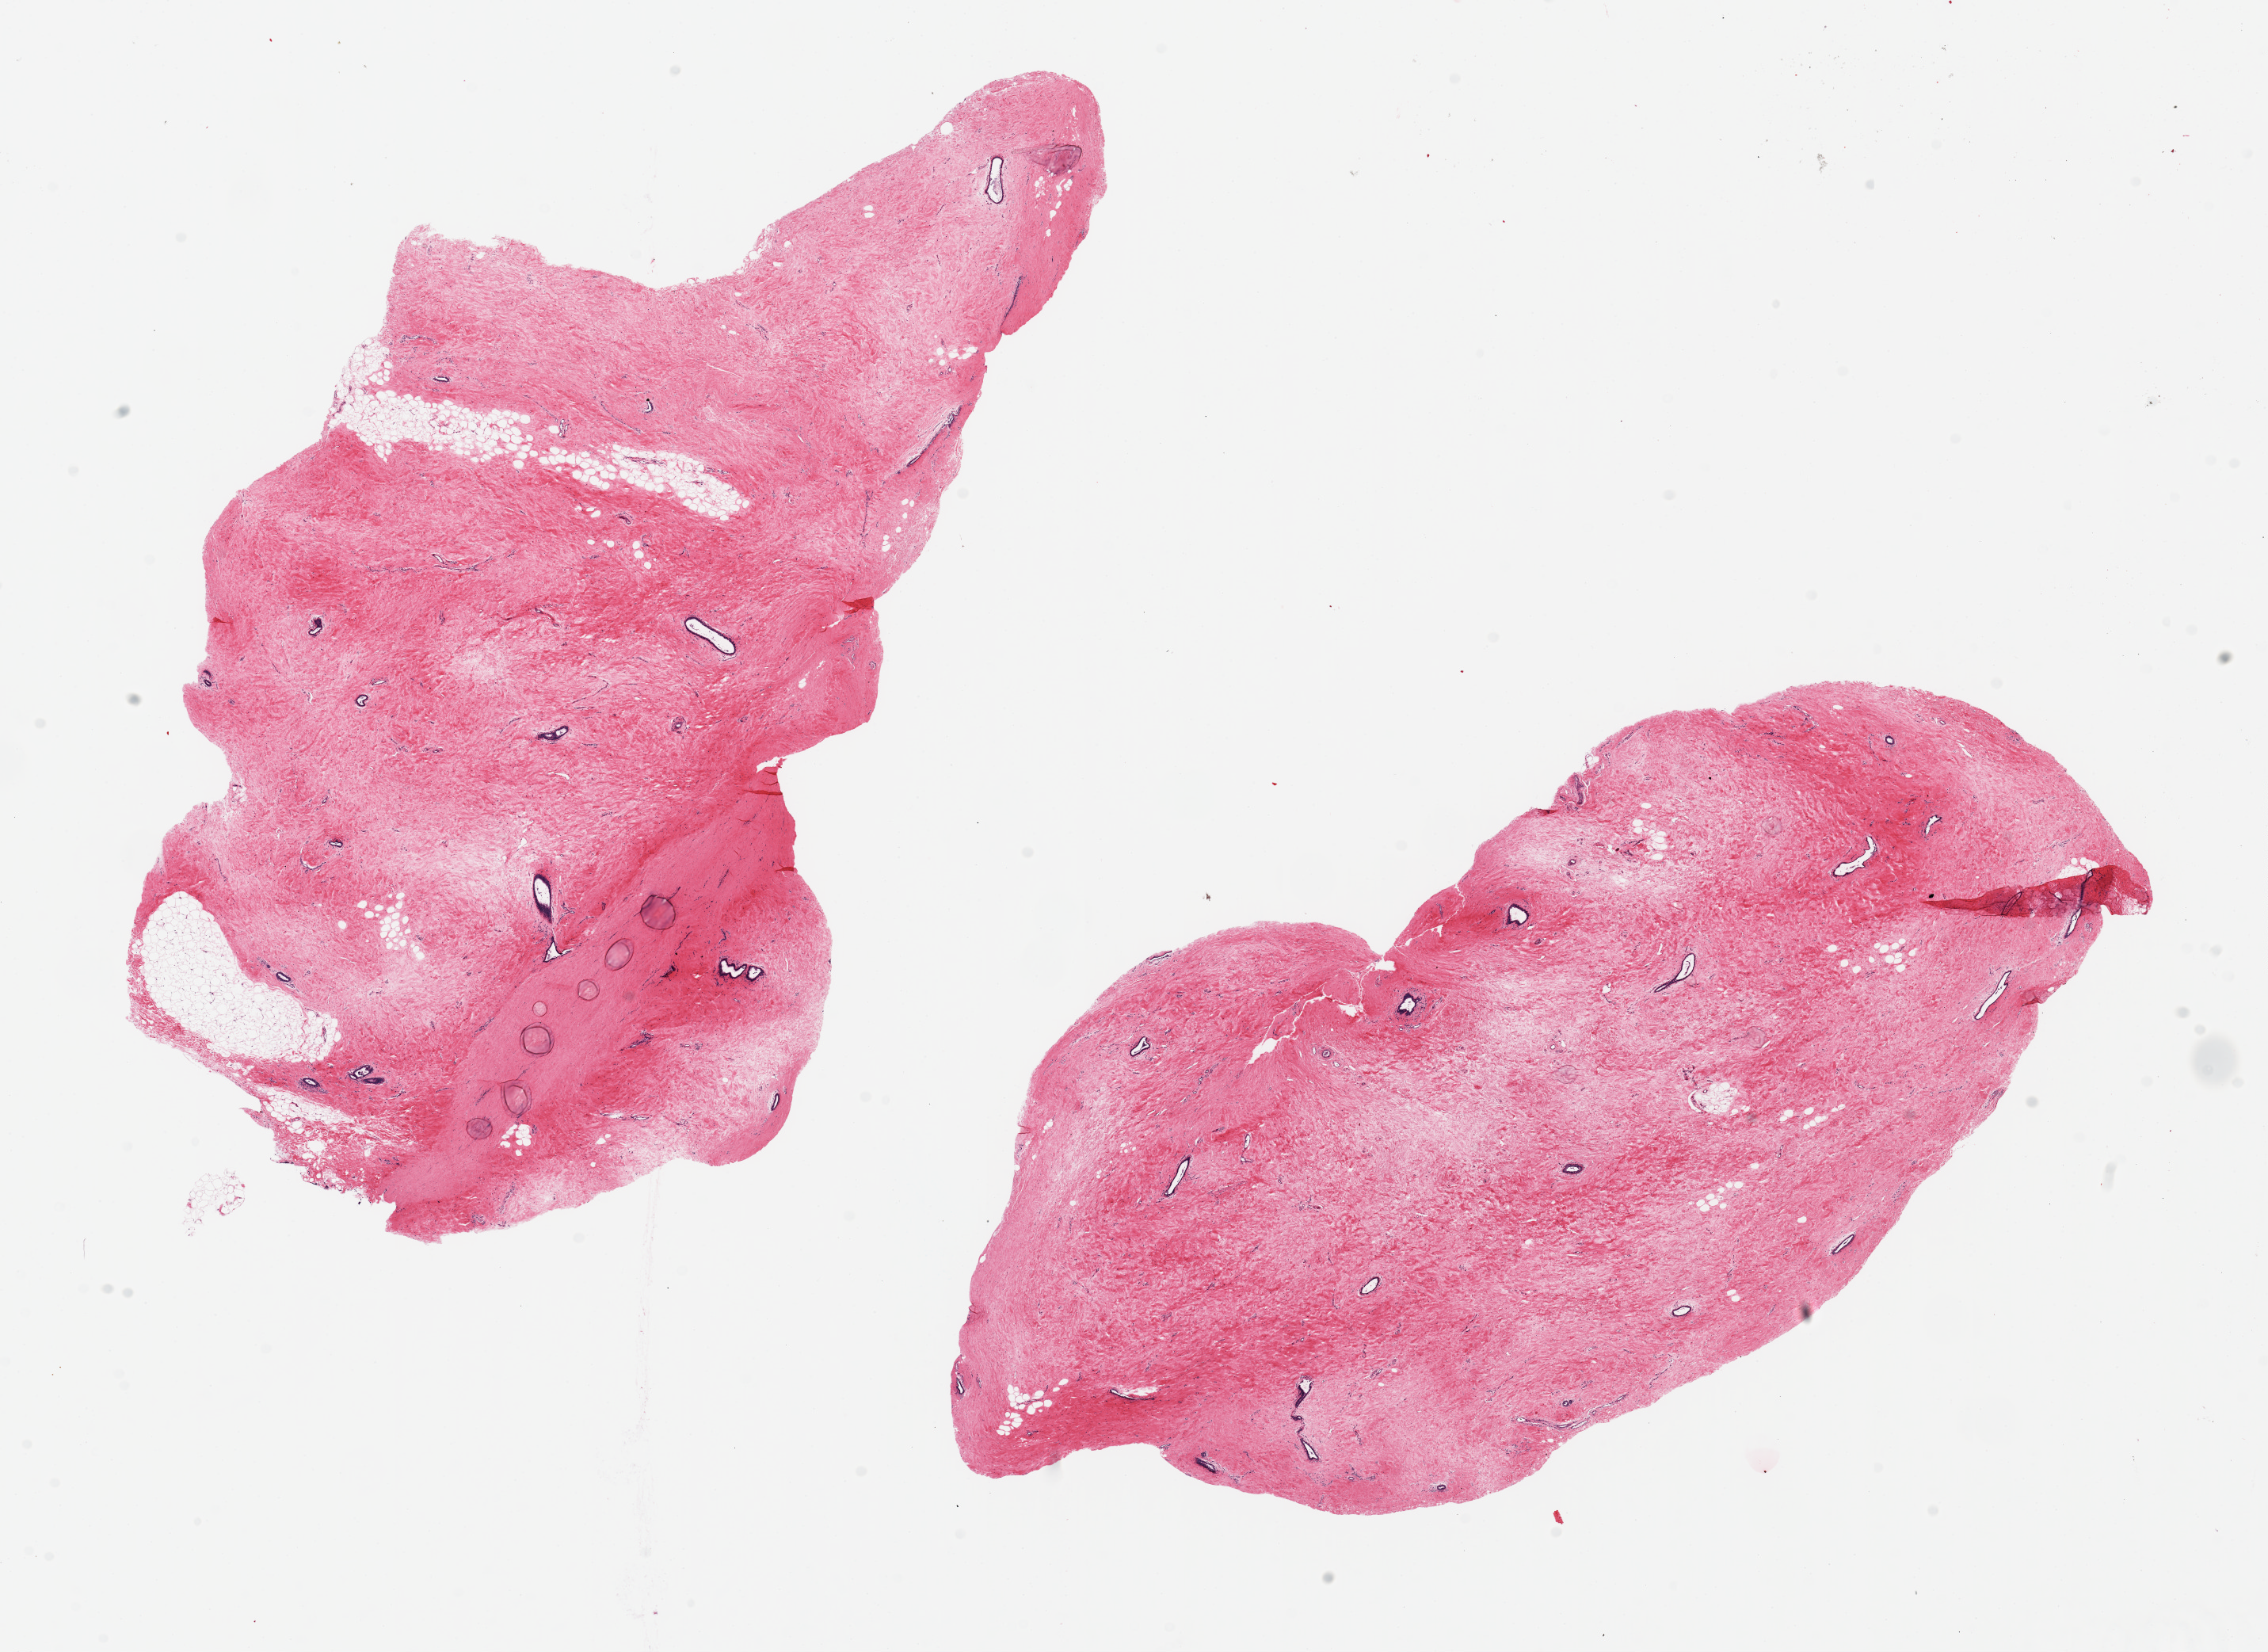
Hematoxylin and eosin (H&E) whole-slide image — whole scanned area (about 22.6 x 16.5 mm, acquisition: 20x scan) shown as a low-resolution overview; PAXgene-fixed, paraffin-embedded tissue; section of breast (target tissue); donor tissue sample. Donor sex: male.
Pathologist's review note for this sample: 2 pieces ~12x6mm; Rare ductal elements noted, some; Mild pseudoangiomatoid stromal hyperplasia noted (PASH).